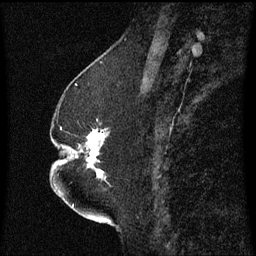
Breast MRI (dynamic contrast-enhanced), one sagittal slice. Slice 24 of 60 in the series (ordered by position). Dynamic contrast-enhanced series, image 2 of 3 at this slice position (ordered by acquisition). 1.5 T. TE 4.2 ms, TR 8.4 ms. 2.3 mm slice thickness. 256 × 256 image matrix. Female patient, age 52 years. Case-level facts recorded for this patient, not image findings: setting: breast cancer imaged before/during neoadjuvant chemotherapy; receptor status: HR-positive, HER2-negative.
Structures marked on this image (semi-automatically segmented with operator editing):
- analysis volume of interest (the breast-tissue region the enhancement analysis was run in; not a lesion): bounding box (x1, y1, x2, y2) in pixels: (65, 120, 111, 183)
- tumour enhancement mask (voxels above the 70 % enhancement threshold inside the analysis volume of interest): (87, 130, 107, 177)